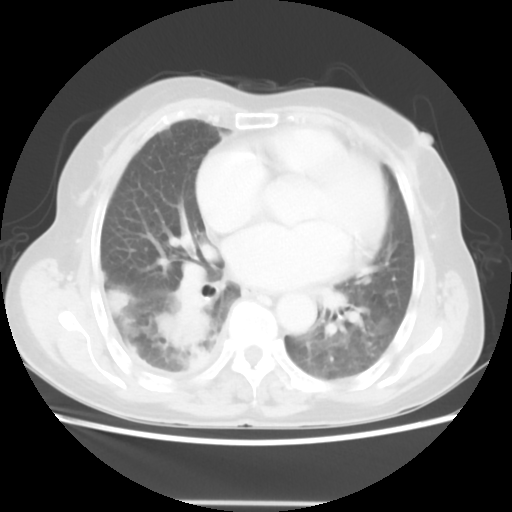
Chest CT, one axial slice. Position 24 of 52 along the scan axis. Reconstruction kernel STANDARD. 140 kVp. Lung window (W 1500 / L -600 HU). 5 mm slice thickness. 512 × 512 image matrix, field of view 337 × 337 mm. Patient: female, 67 years. Case-level facts recorded for this patient, not image findings: clinical TNM (as recorded): T3 N1 M1.
Structures marked on this image (rectangle marked by the reading radiologist):
- lung tumour (recorded histology: adenocarcinoma): box from (x=154, y=303) to (x=217, y=375) px